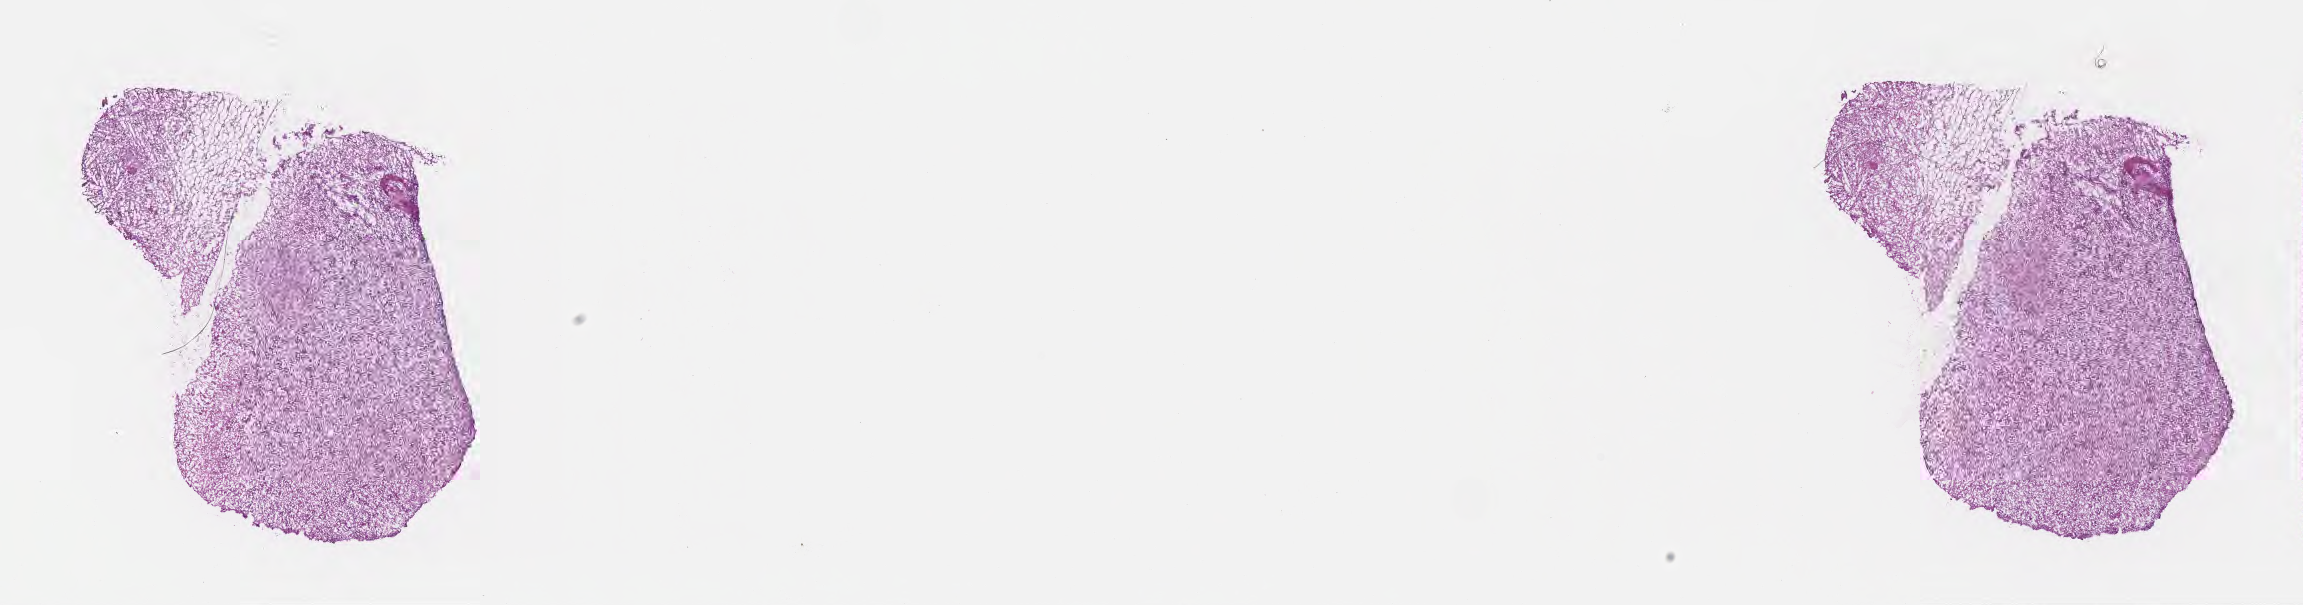
Haematoxylin and eosin whole-slide image, low-resolution overview of the scanned area, about 18.6 x 4.9 mm. Frozen section (snap frozen). Primary tumor. Anatomic site: brain. Male, age 58 years at initial diagnosis. Slide review estimates, as recorded: tumor cells 28%, tumor nuclei 57%, stromal cells 40%, necrosis 11%, normal cells 21%. Inflammatory infiltration, as recorded: lymphocyte infiltration 0%, monocyte infiltration 0%, neutrophil infiltration 0%.
Diagnosis: Glioblastoma, NOS.